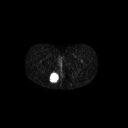
FDG PET of an extremity soft-tissue mass (from a PET/CT study), one axial slice. Slice 26 of 267 in the series (ordered by position). 128 × 128 image matrix, field of view 700 × 700 mm. Patient: female, 17 years. Case-level facts recorded for this patient, not image findings: histological type: epithelioid sarcoma; grade: intermediate; site of the primary tumour: right buttock.
Annotated regions visible in this slice (expert contour drawn on MRI and transferred to this co-registered scan by the dataset authors):
- gross tumour volume including surrounding oedema: bounding box <48,71,59,83> (left, top, right, bottom; pixels)
- gross tumour volume (mass): <49,72,59,82>